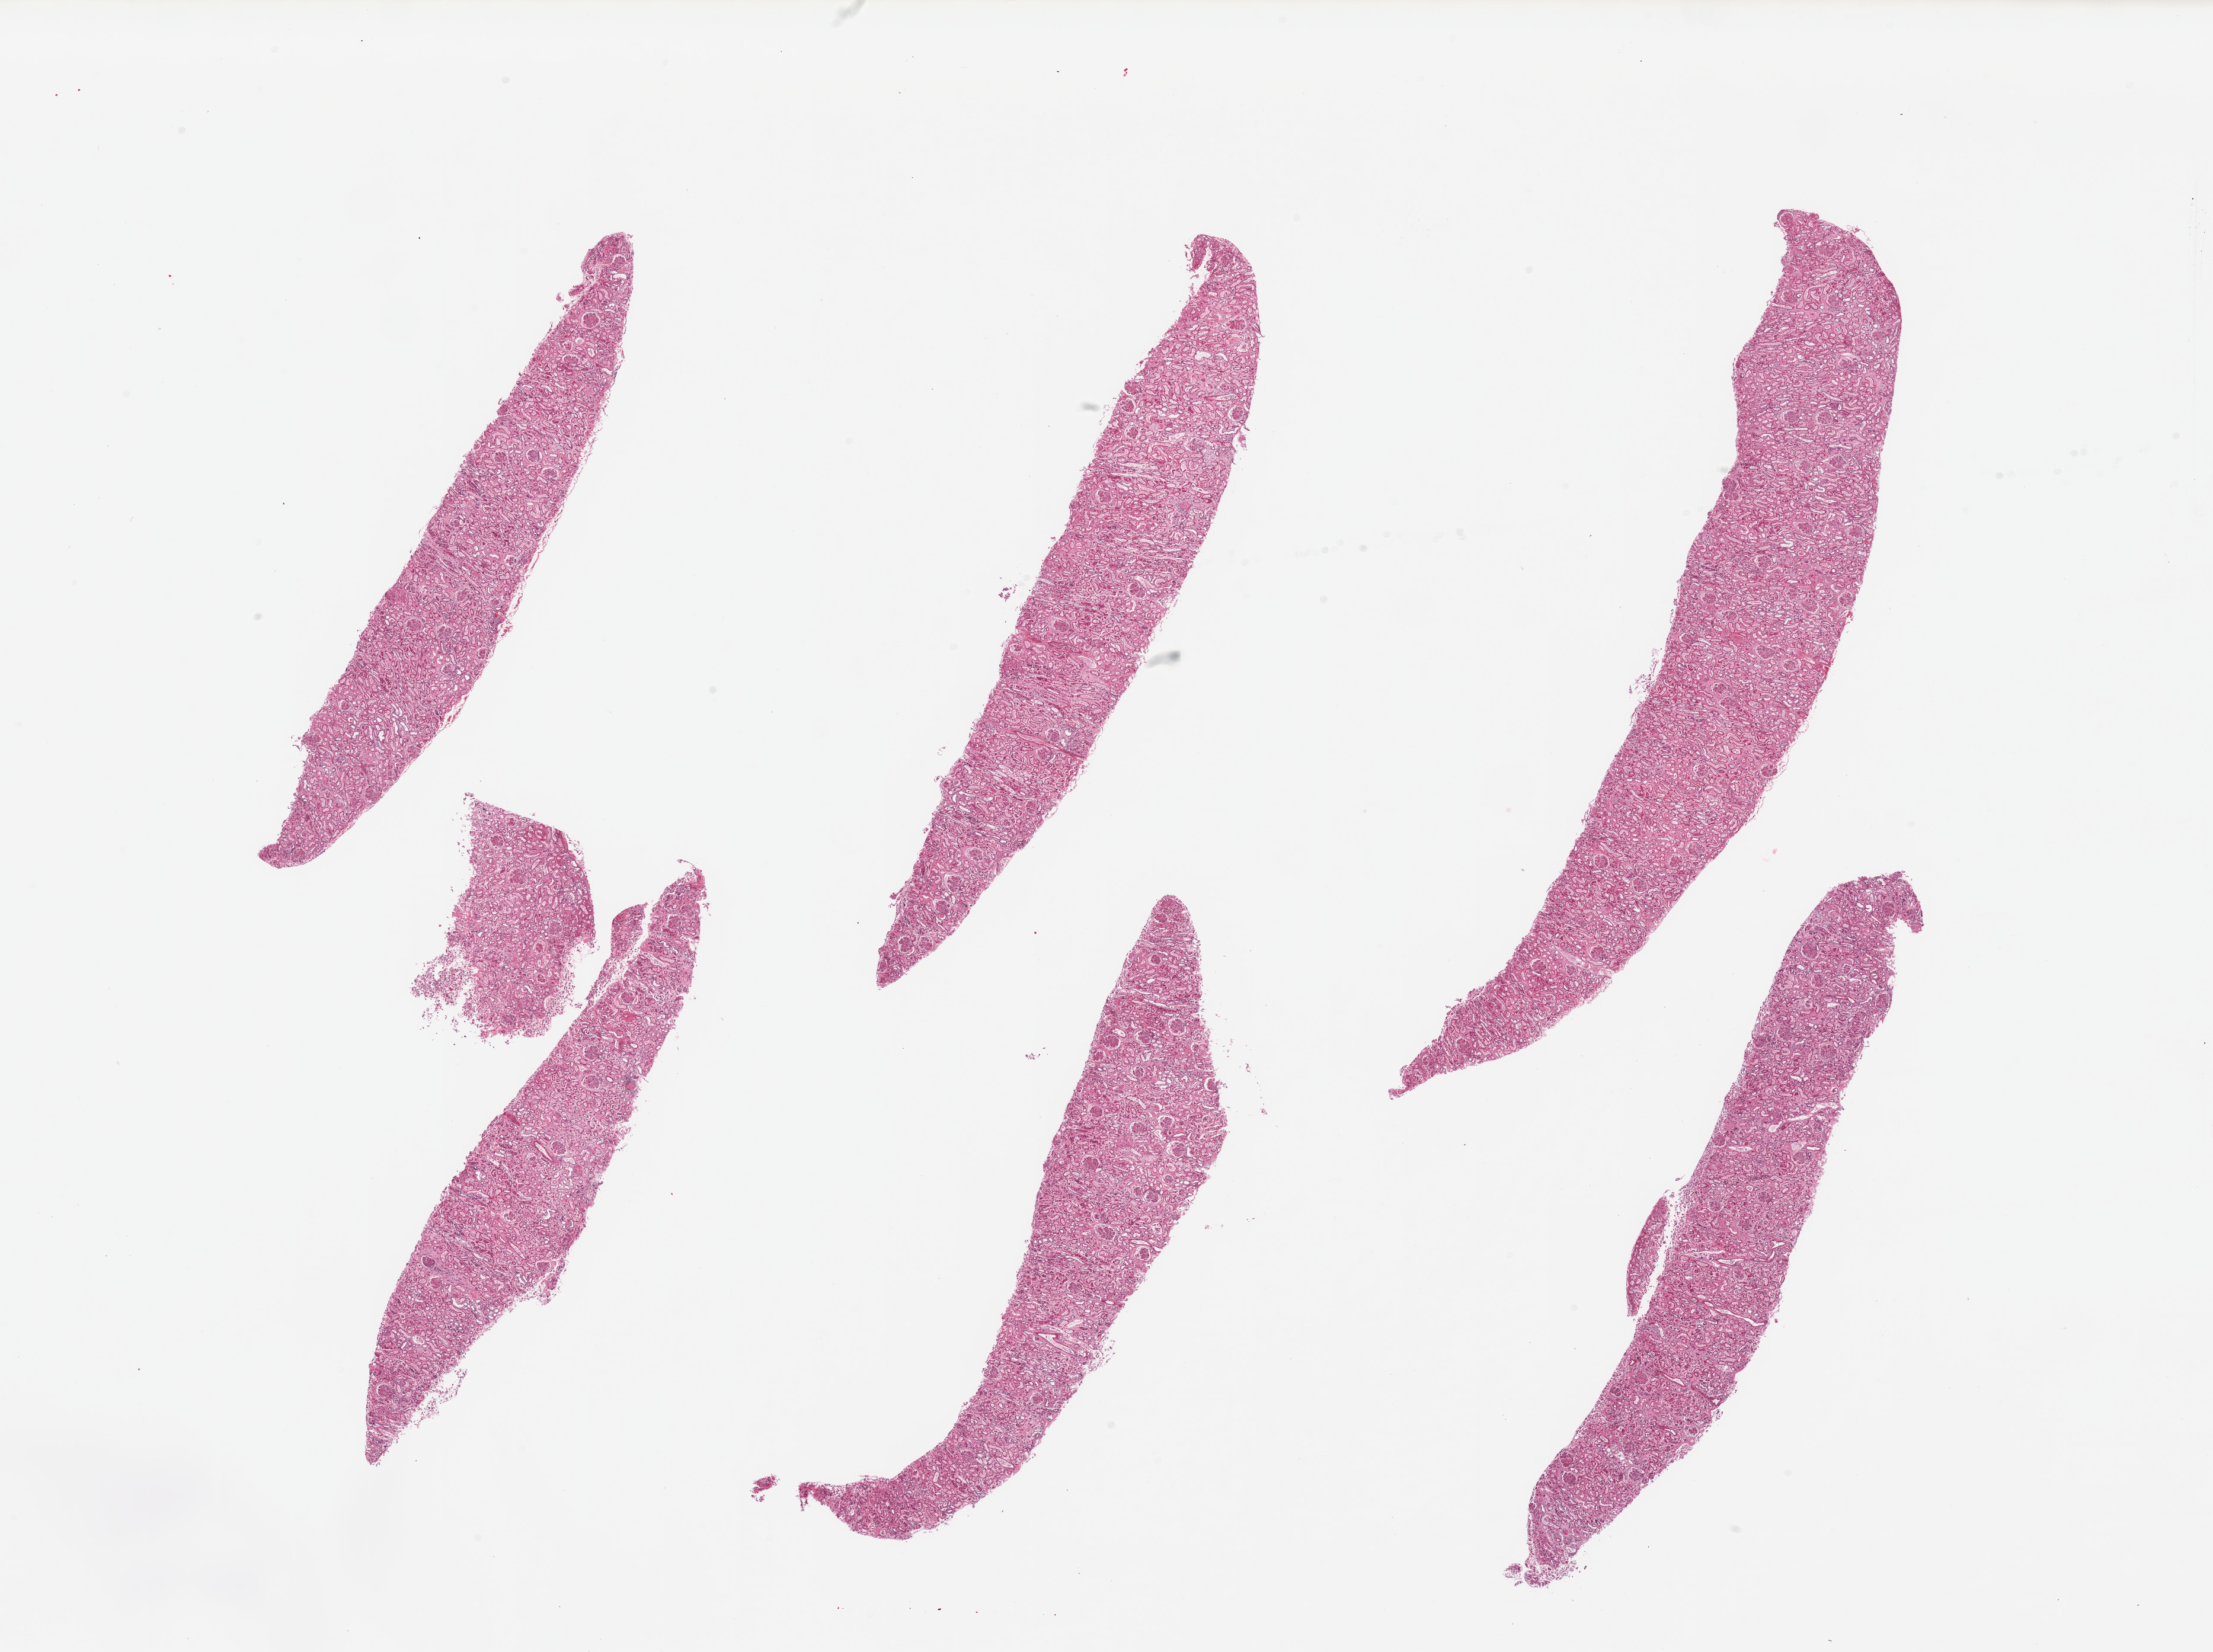
Whole-slide image, H&E stain, brightfield — low-resolution overview of the scanned area, about 29.5 x 22.1 mm (slide scanned at 20x); PAXgene-fixed paraffin-embedded (PFPE) section; section of renal cortex (target tissue); tissue donor sample. Male donor.
Reviewer comment on this tissue sample: 6 pieces; tubules mostly affected by autolysis; no sign of chronic disease.